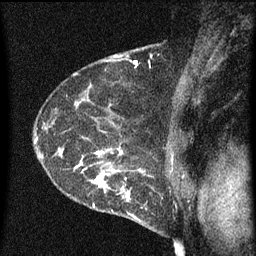
Breast MRI (dynamic contrast-enhanced), one sagittal slice; position 46 of 60 along the scan axis; dynamic contrast-enhanced series, image 2 of 3 at this slice position (ordered by acquisition); 1.5 T; TE 4.2 ms, TR 8 ms; 2 mm slice thickness; 256 × 256 image matrix, field of view 180 × 180 mm. Female patient, age 54 years.
Annotated regions visible in this slice (semi-automatic segmentation, software-assisted and operator-edited):
- analysis volume of interest (the breast-tissue region the enhancement analysis was run in; not a lesion): bounding box <49,138,164,209> (left, top, right, bottom; pixels)
- tumour enhancement mask (voxels above the 70 % enhancement threshold inside the analysis volume of interest): <61,146,148,209>